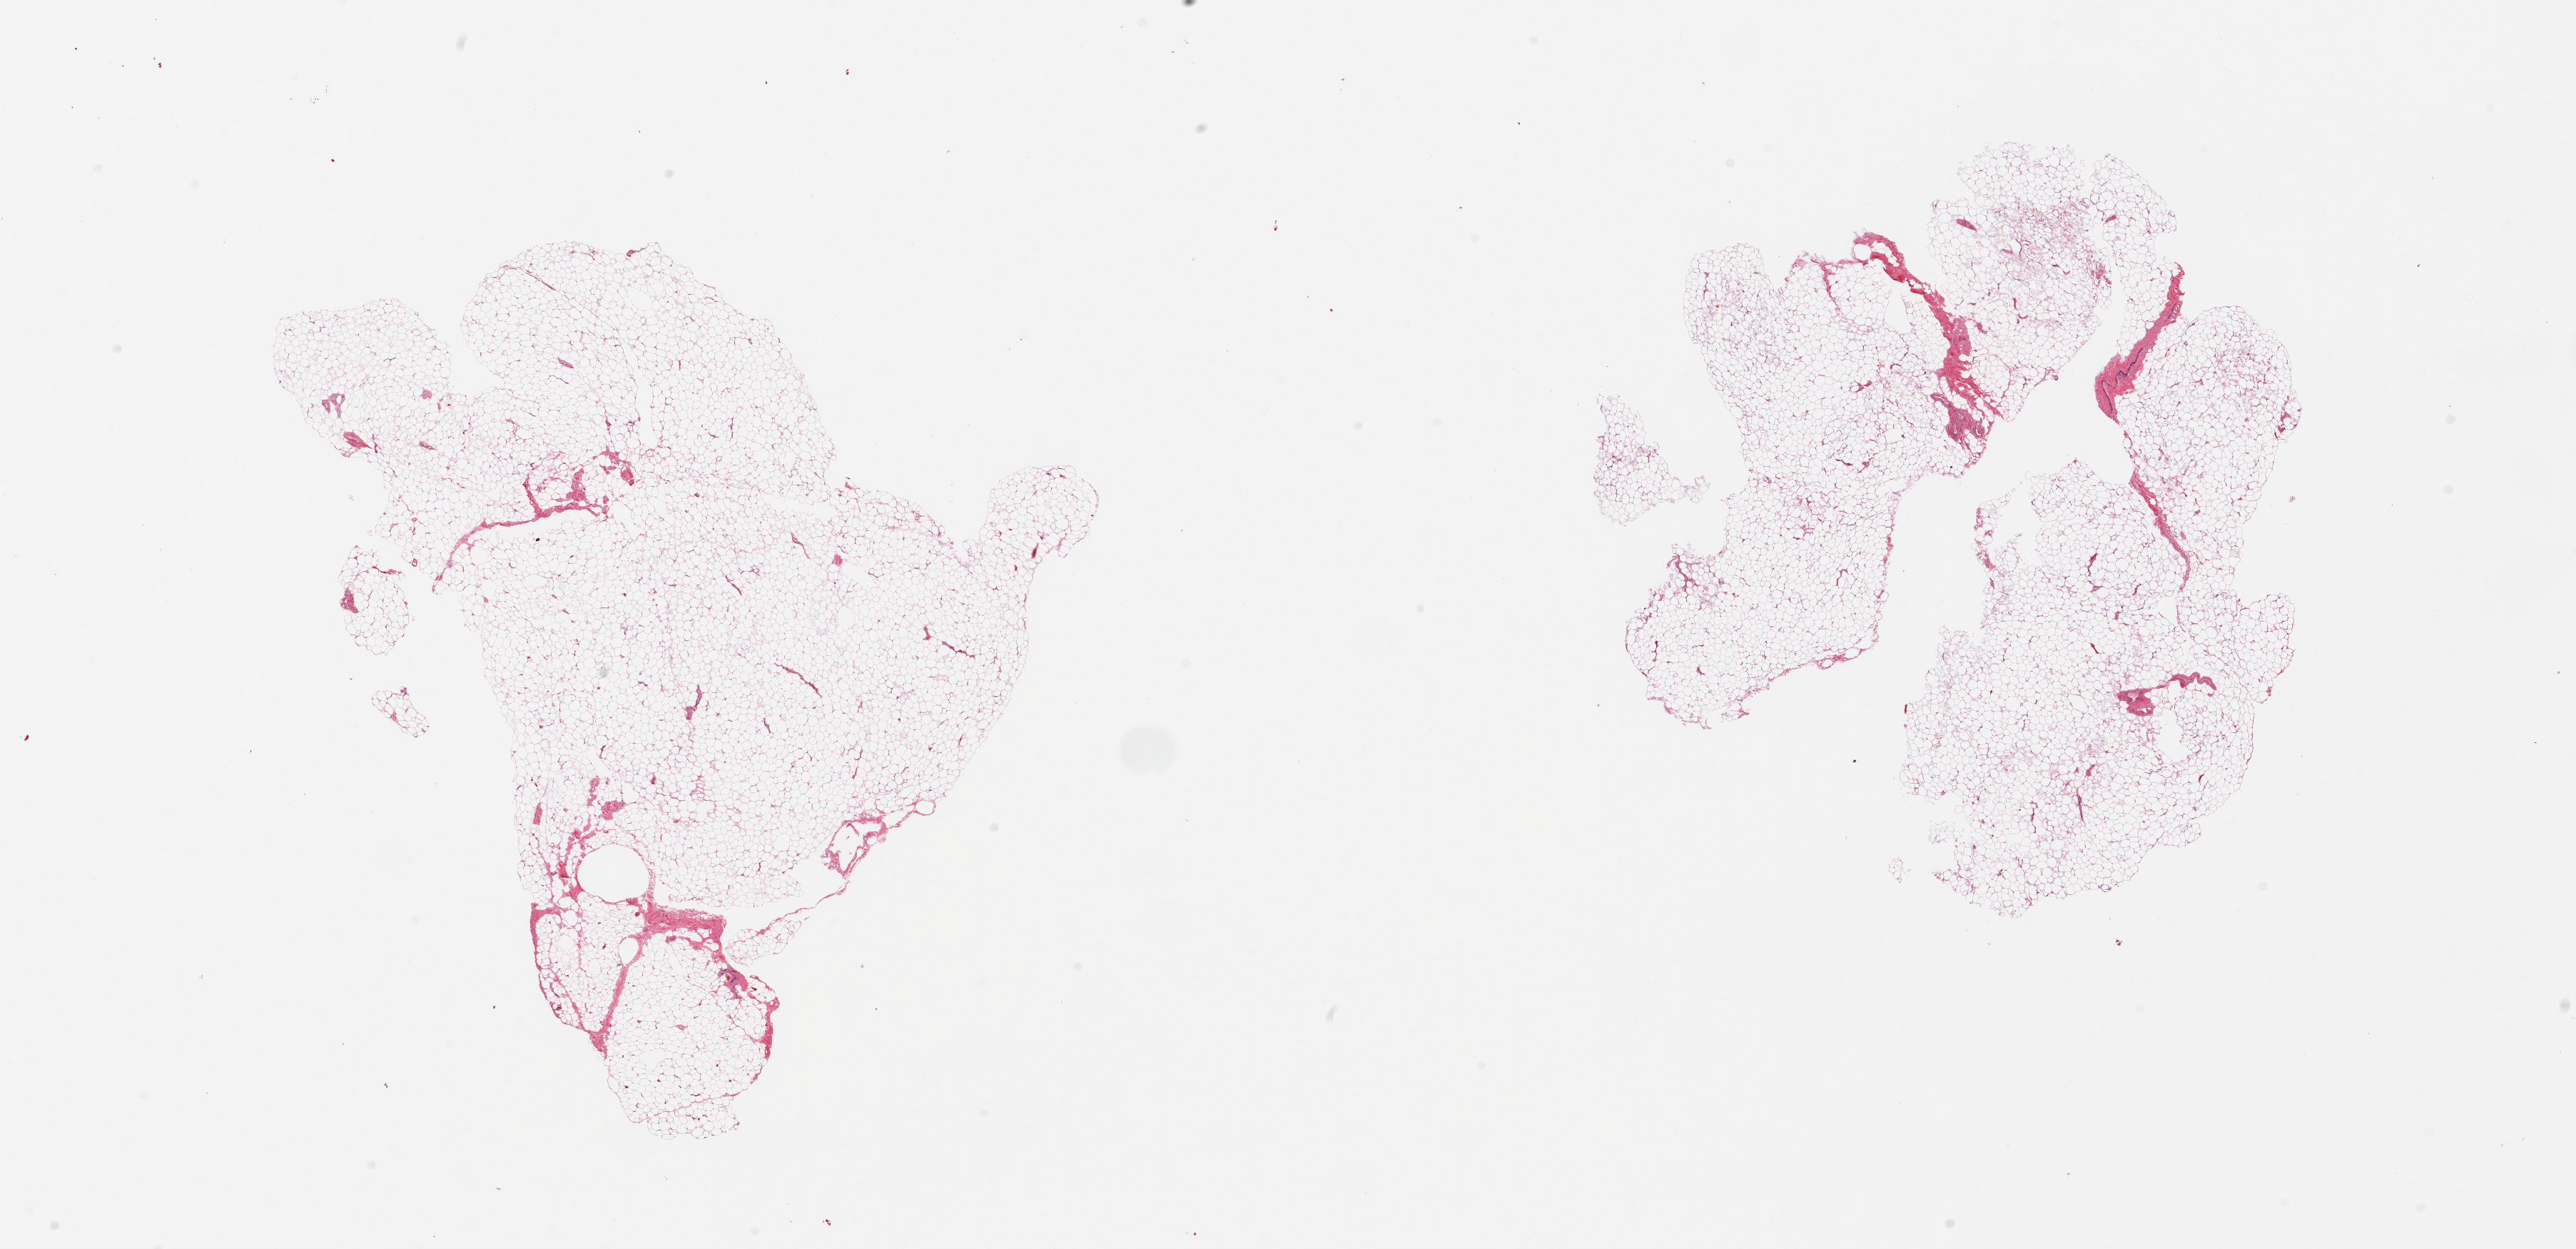
Whole-slide image, H&E stain, brightfield, a low-resolution overview of the entire scanned area, about 28.5 x 13.8 mm; PAXgene-fixed paraffin-embedded (PFPE) section; section of breast (target tissue); donor tissue sample. Donor sex: female.
Review note (as recorded): 2 pieces; mostly fat with minute atrophic ducts.